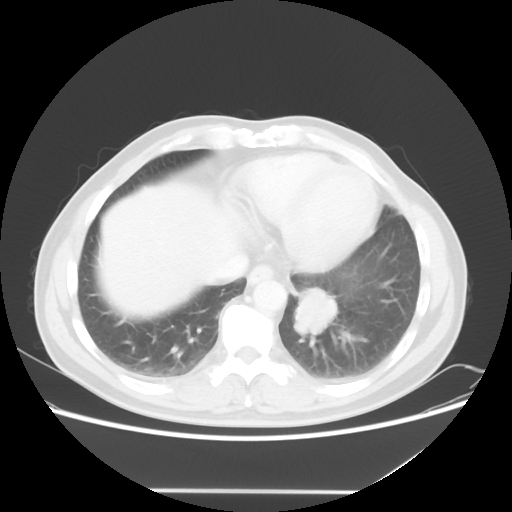
Chest CT, one axial slice. Position 16 of 56 along the scan axis. Reconstruction kernel STANDARD. 120 kVp. Lung window (W 1500 / L -600 HU). 512 × 512 image matrix, field of view 385 × 385 mm. Patient: male, 61 years. Case-level facts recorded for this patient, not image findings: clinical TNM (as recorded): T1c N0 M0; histopathological grade: G3.
Outlined on this slice (bounding box drawn by a radiologist):
- lung tumour (recorded histology: adenocarcinoma): bounding box [x1, y1, x2, y2] px = [288, 283, 348, 345]